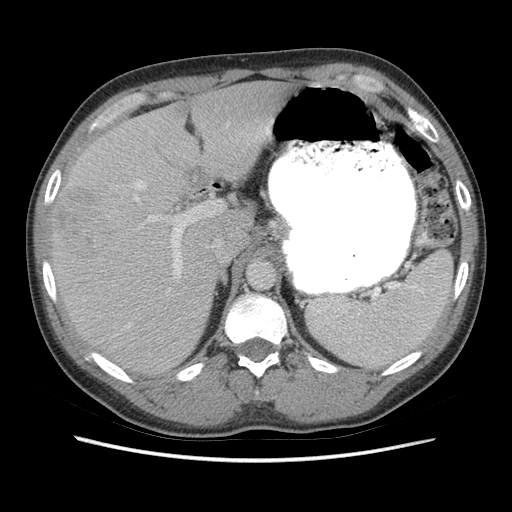
Contrast-enhanced abdominal CT (liver protocol), one axial slice; position 44 of 73 along the scan axis; 140 kVp; soft-tissue window (W 400 / L 40 HU); 512 × 512 image matrix, field of view 360 × 360 mm. From the clinical record (not read from this slice): diagnosis: hepatocellular carcinoma (patient treated with transarterial chemoembolisation; whether this scan precedes or follows treatment is not stated here); TNM stage (as recorded): Stage-IIIA; Child-Pugh class: A.
Outlined on this slice (semi-automatically segmented with operator editing):
- liver parenchyma outside the tumour (the mass and vessels are separate outlines, so this box may not span the whole liver): bounding box [x1, y1, x2, y2] px = [51, 80, 292, 374]
- mass: [56, 187, 113, 257]
- liver vessels: [127, 120, 273, 328]